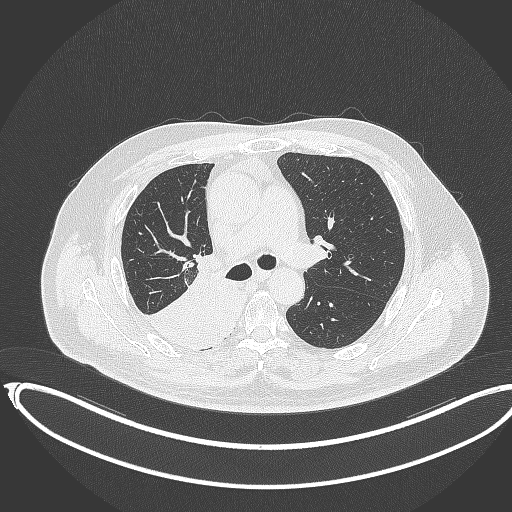
Chest CT, one axial slice; reconstruction kernel B70f; 120 kVp; lung window (W 1500 / L -600 HU); 1 mm slice thickness; 512 × 512 image matrix, field of view 436 × 436 mm. Patient: male, 68 years. Case-level facts recorded for this patient, not image findings: clinical TNM (as recorded): T2a N0 M0.
Annotated regions visible in this slice (bounding box drawn by a radiologist):
- lung tumour (recorded histology: adenocarcinoma): box from (x=141, y=261) to (x=232, y=345) px